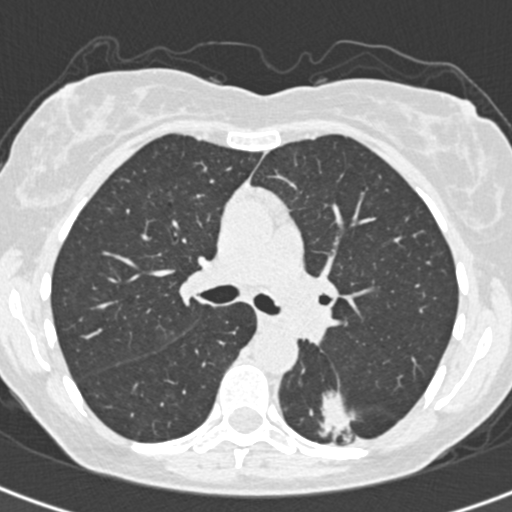
Low-dose screening chest CT, one axial slice; lung window (W 1500 / L -600 HU); 512 × 512 image matrix, field of view 284 × 284 mm.
Annotated regions visible in this slice (manually delineated by an expert):
- lesion 1 (tumor, lower lobe of left lung): bounding box [x1, y1, x2, y2] px = [321, 391, 354, 441]